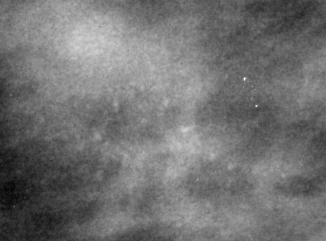
Cropped region of a digitized screen-film mammogram centred on a radiologist-marked abnormality; left breast; MLO view; BI-RADS breast density category 4 (scale 1–4).
Marked abnormality: calcifications, morphology pleomorphic, distribution clustered; BI-RADS assessment category 4; pathology (as recorded): malignant.